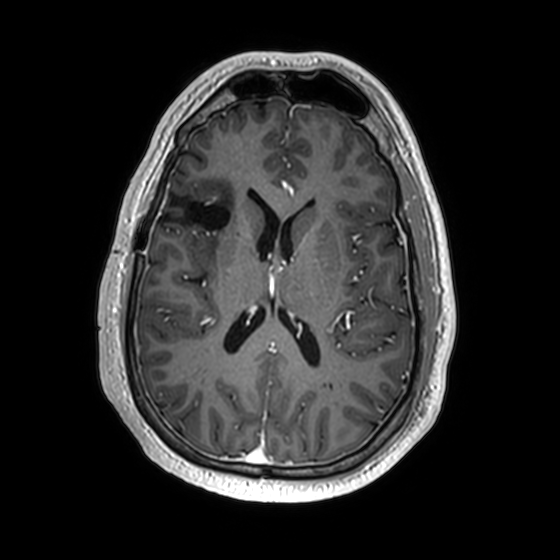
Brain MRI from a brain-tumour surgery series, one axial slice; position 79 of 174 along the scan axis; T1-weighted post-contrast; 1 mm slice thickness; 560 × 560 image matrix, field of view 256 × 256 mm. From the clinical record (not read from this slice): histopathology: Astrocytoma; WHO grade: 2; IDH mutation: yes; tumour location: Right Insular.
Annotated regions visible in this slice (expert manual segmentation):
- previous resection cavity: box from (x=158, y=196) to (x=230, y=230) px